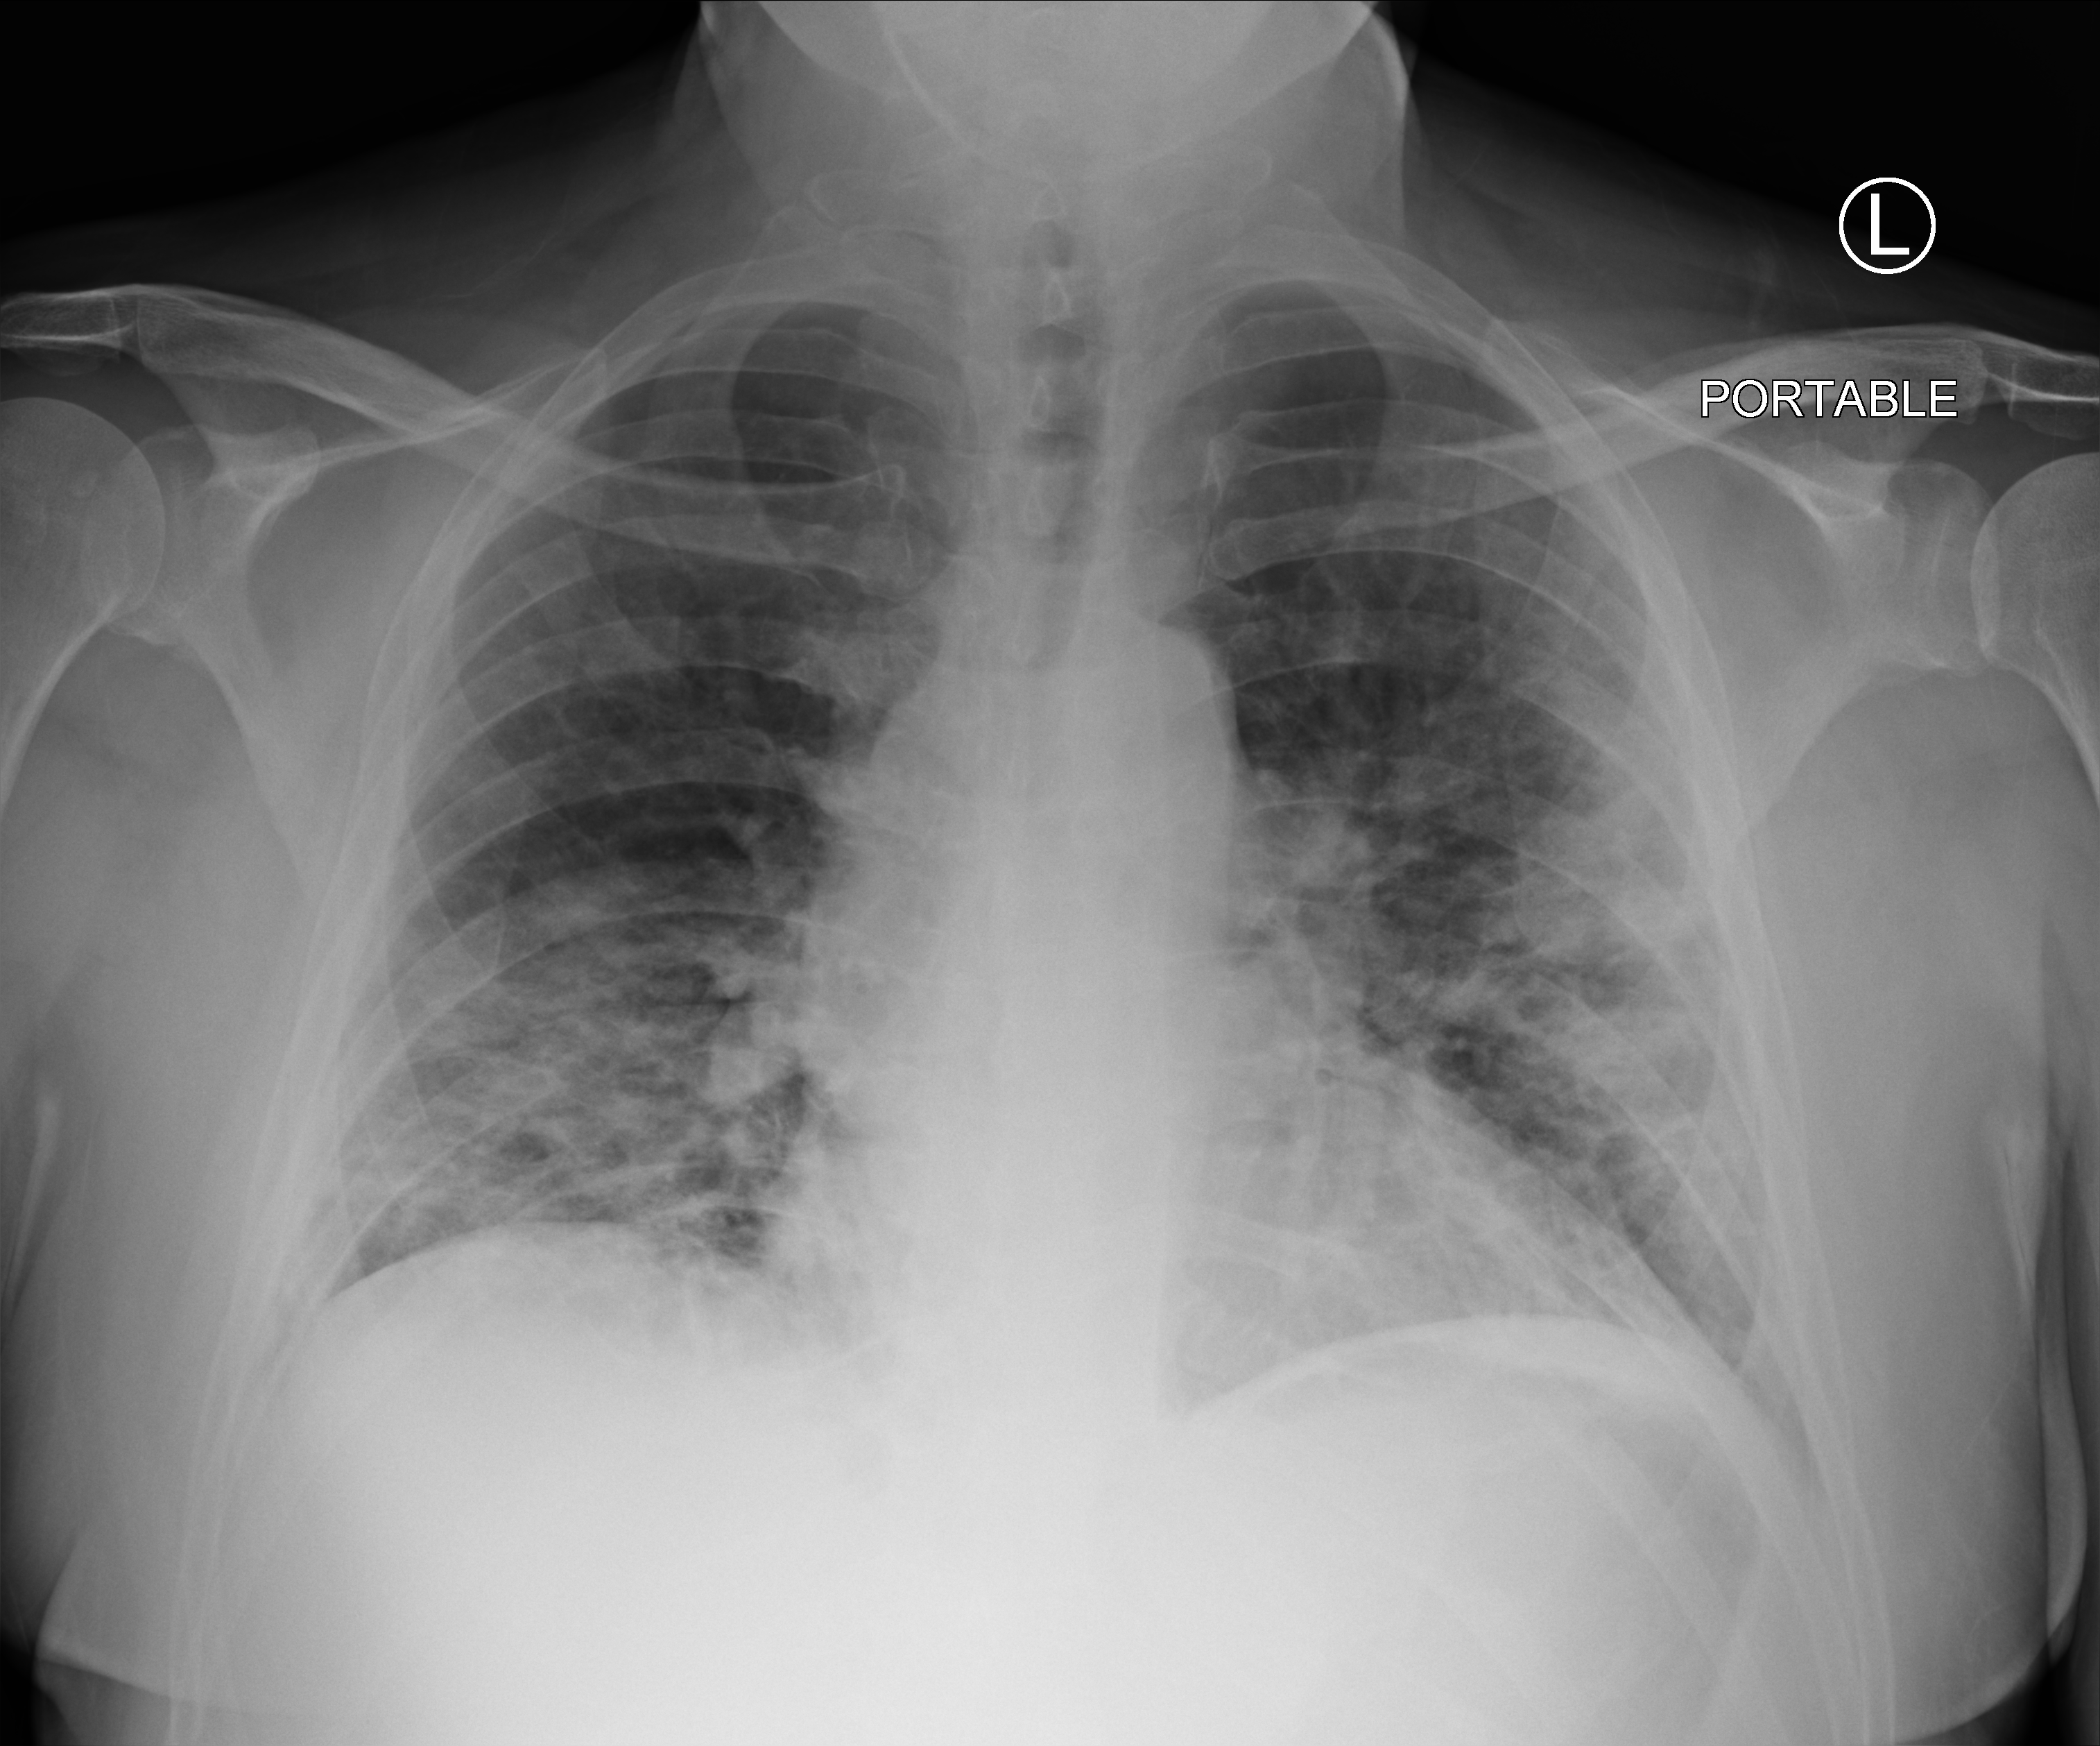
Bedside chest radiograph (computed radiography), anteroposterior (AP) projection. Male patient hospitalised with COVID-19, age 18–59 years.
Hospital-stay facts (about this admission, not read from this image; timing relative to this image not recorded):
- mechanically ventilated during this hospital stay: no
- admitted to intensive care during this hospital stay: no